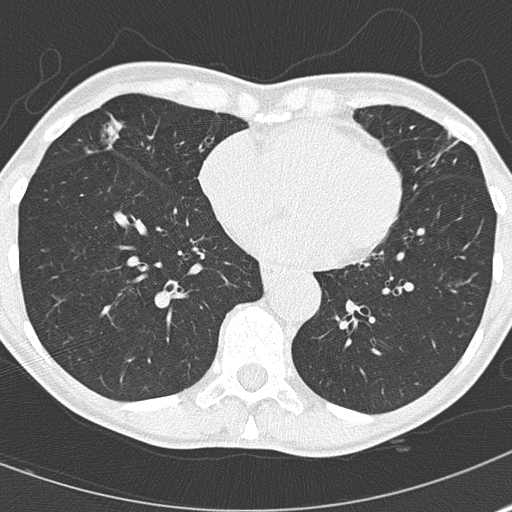
Axial slice from a low-dose chest CT screening exam; second screening round (one year after baseline); lung window (W 1500 / L -600 HU); 2 mm slice thickness; lung (sharp) reconstruction kernel (B50f); 120 kVp; slice 110 of 167 in the series. Female, age 67 years at enrolment. Current smoker at enrolment.
Expert reader's lesion annotation, bounding box (x1, y1, x2, y2) in pixels: (84, 104, 194, 194). The screening reader recorded 2 non-calcified nodules or masses ≥4 mm on this exam; which of them this box marks is not recorded. Official screen result: positive, other. Lung cancer was diagnosed 475 days after this screen: bronchiolo-alveolar adenocarcinoma, NOS, right middle lobe, well differentiated (G1), stage IA (AJCC 6th edition), 25 mm at pathology.